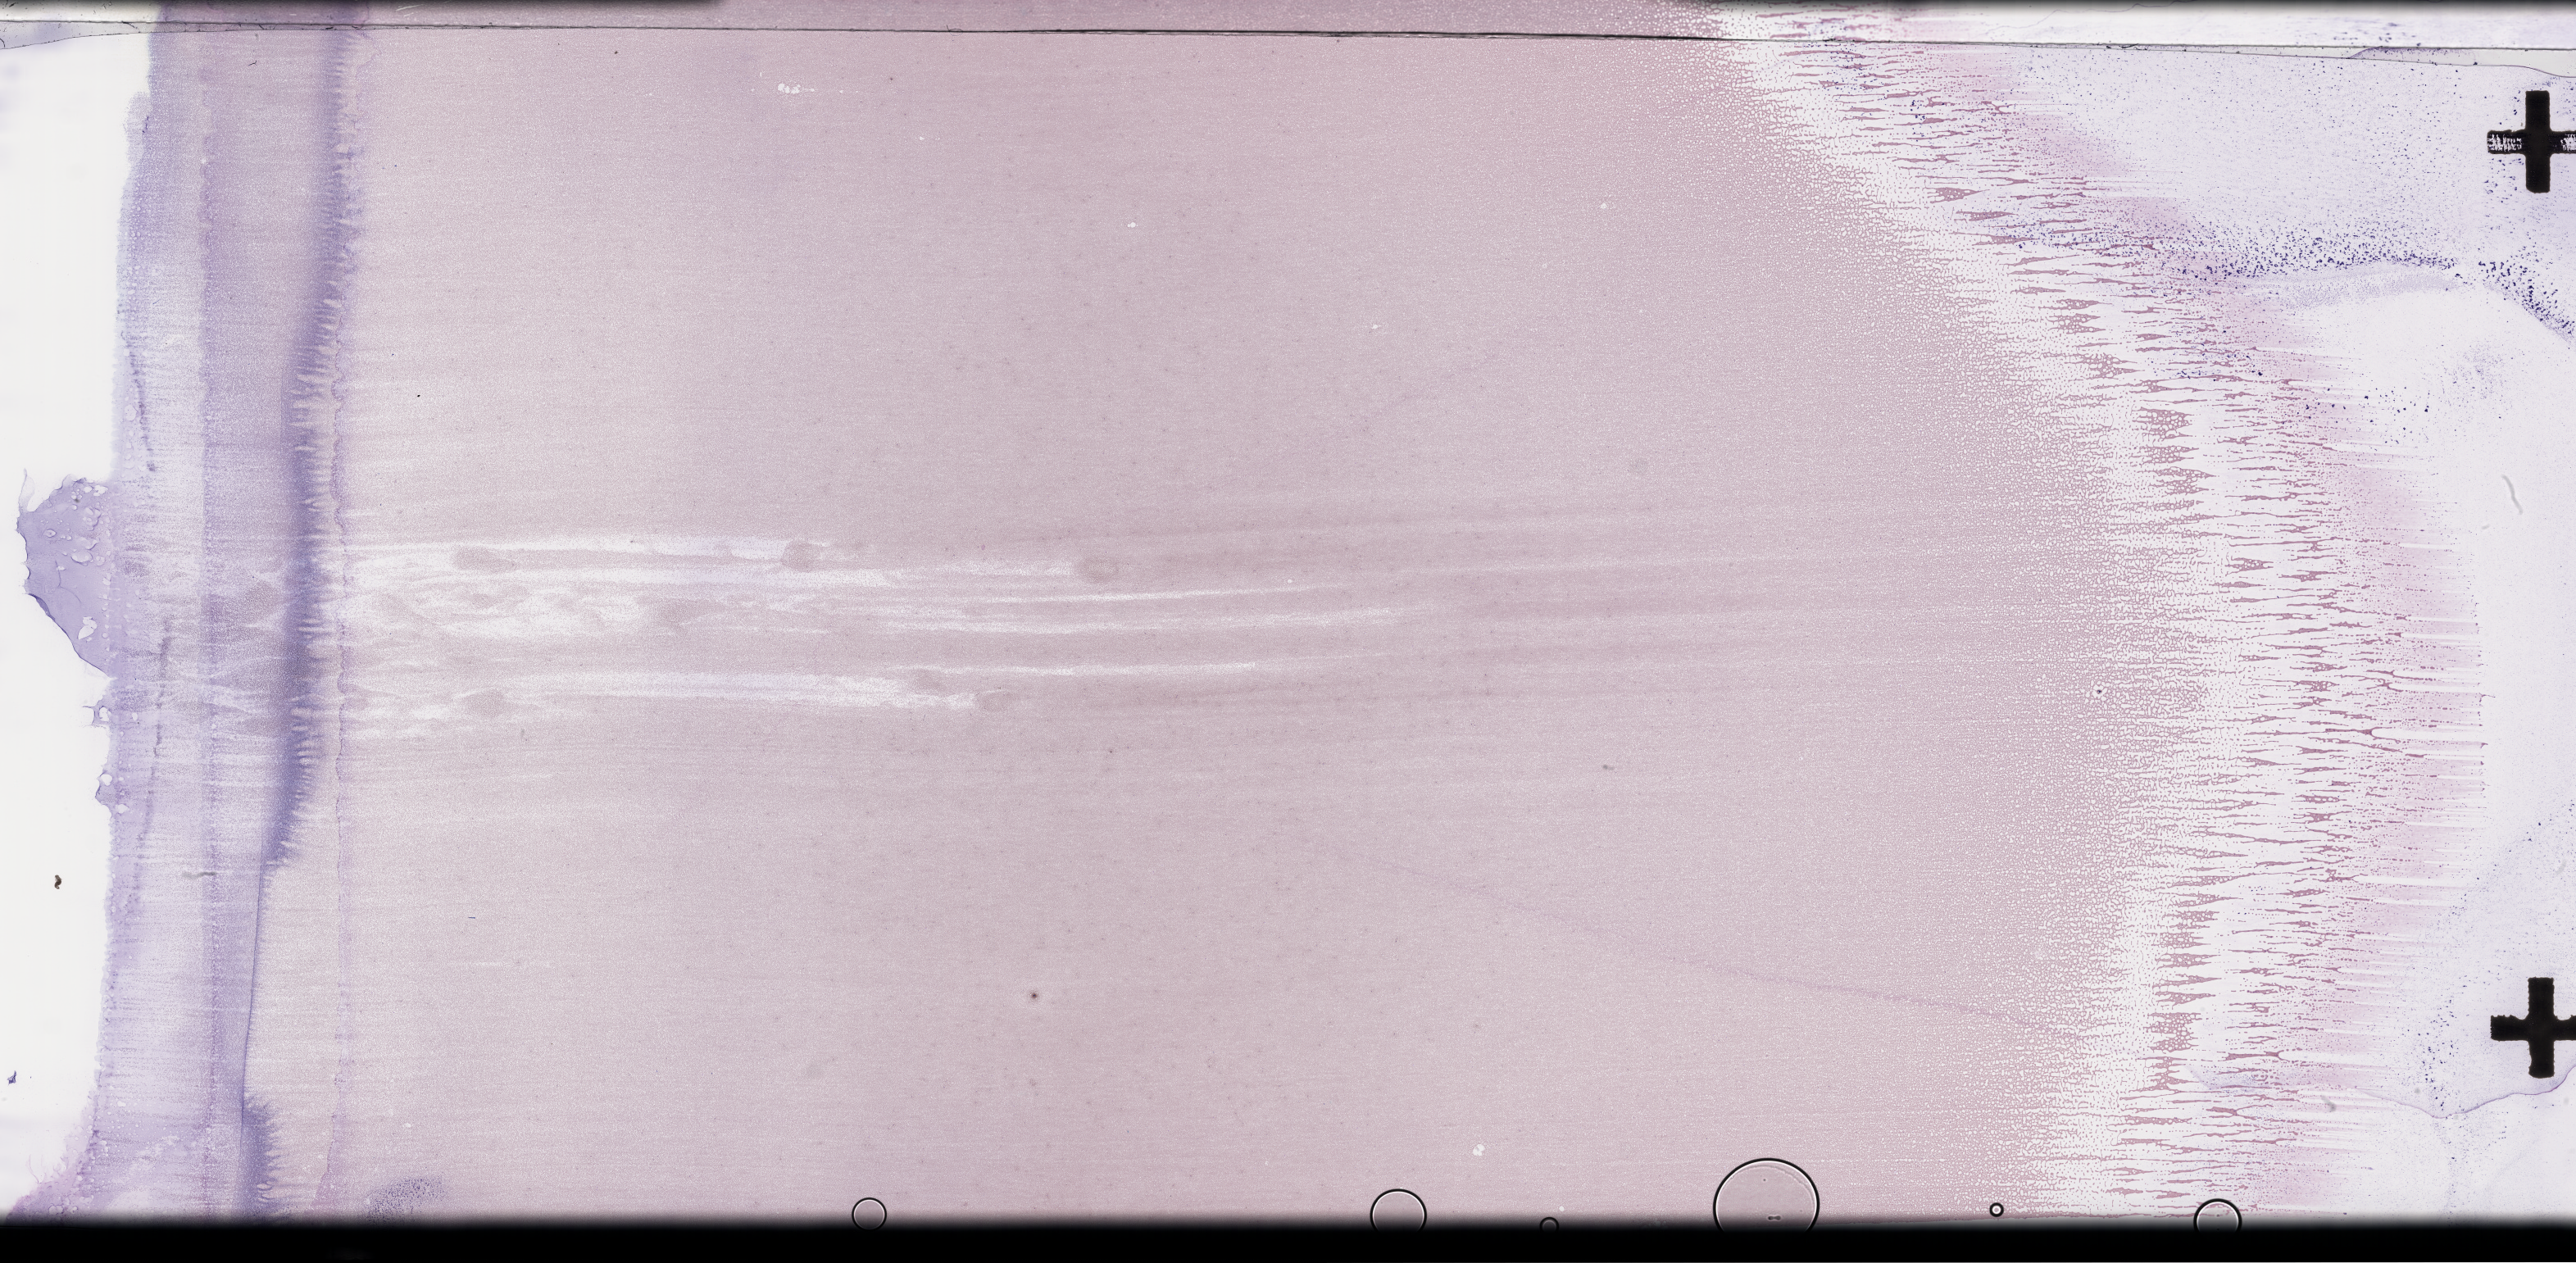
Whole-slide image of a whole blood smear, Wright–Giemsa stain, shown as a low-resolution overview of the whole scanned area (about 50.8 x 24.9 mm). EDTA-anticoagulated smear. Female patient.
From a patient with: Plasma Cell Myeloma.